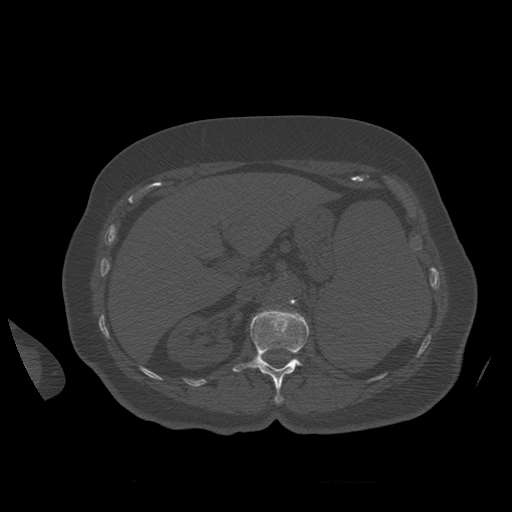
CT including the spine, one axial slice. Slice 276 of 399 in the series (ordered by position). 120 kVp. Bone window (W 1800 / L 400 HU). 1.25 mm slice thickness. 512 × 512 image matrix. Patient age 81 years. Case-level facts recorded for this patient, not image findings: primary cancer: renal.
Annotated regions visible in this slice (semi-automatically segmented with operator editing):
- L1 vertebra: bounding box <233,309,310,404> (left, top, right, bottom; pixels)